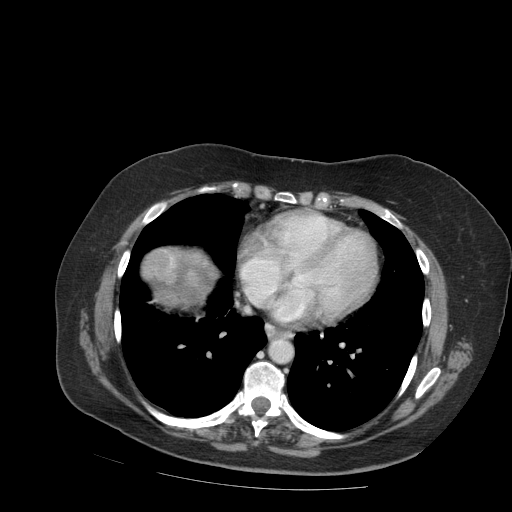
Contrast-enhanced abdominal CT (liver protocol), one axial slice. Slice 90 of 99 in the series (ordered by position). Reconstruction kernel STANDARD. Soft-tissue window (W 400 / L 40 HU). 2.5 mm slice thickness. 512 × 512 image matrix. From the clinical record (not read from this slice): diagnosis: hepatocellular carcinoma (patient treated with transarterial chemoembolisation; whether this scan precedes or follows treatment is not stated here); TNM stage (as recorded): Stage-IVB; Child-Pugh class: A; tumour differentiation: moderately differentiated.
Annotated regions visible in this slice (semi-automatic segmentation, software-assisted and operator-edited):
- liver parenchyma outside the tumour (the mass and vessels are separate outlines, so this box may not span the whole liver): bounding box <142,246,216,308> (left, top, right, bottom; pixels)